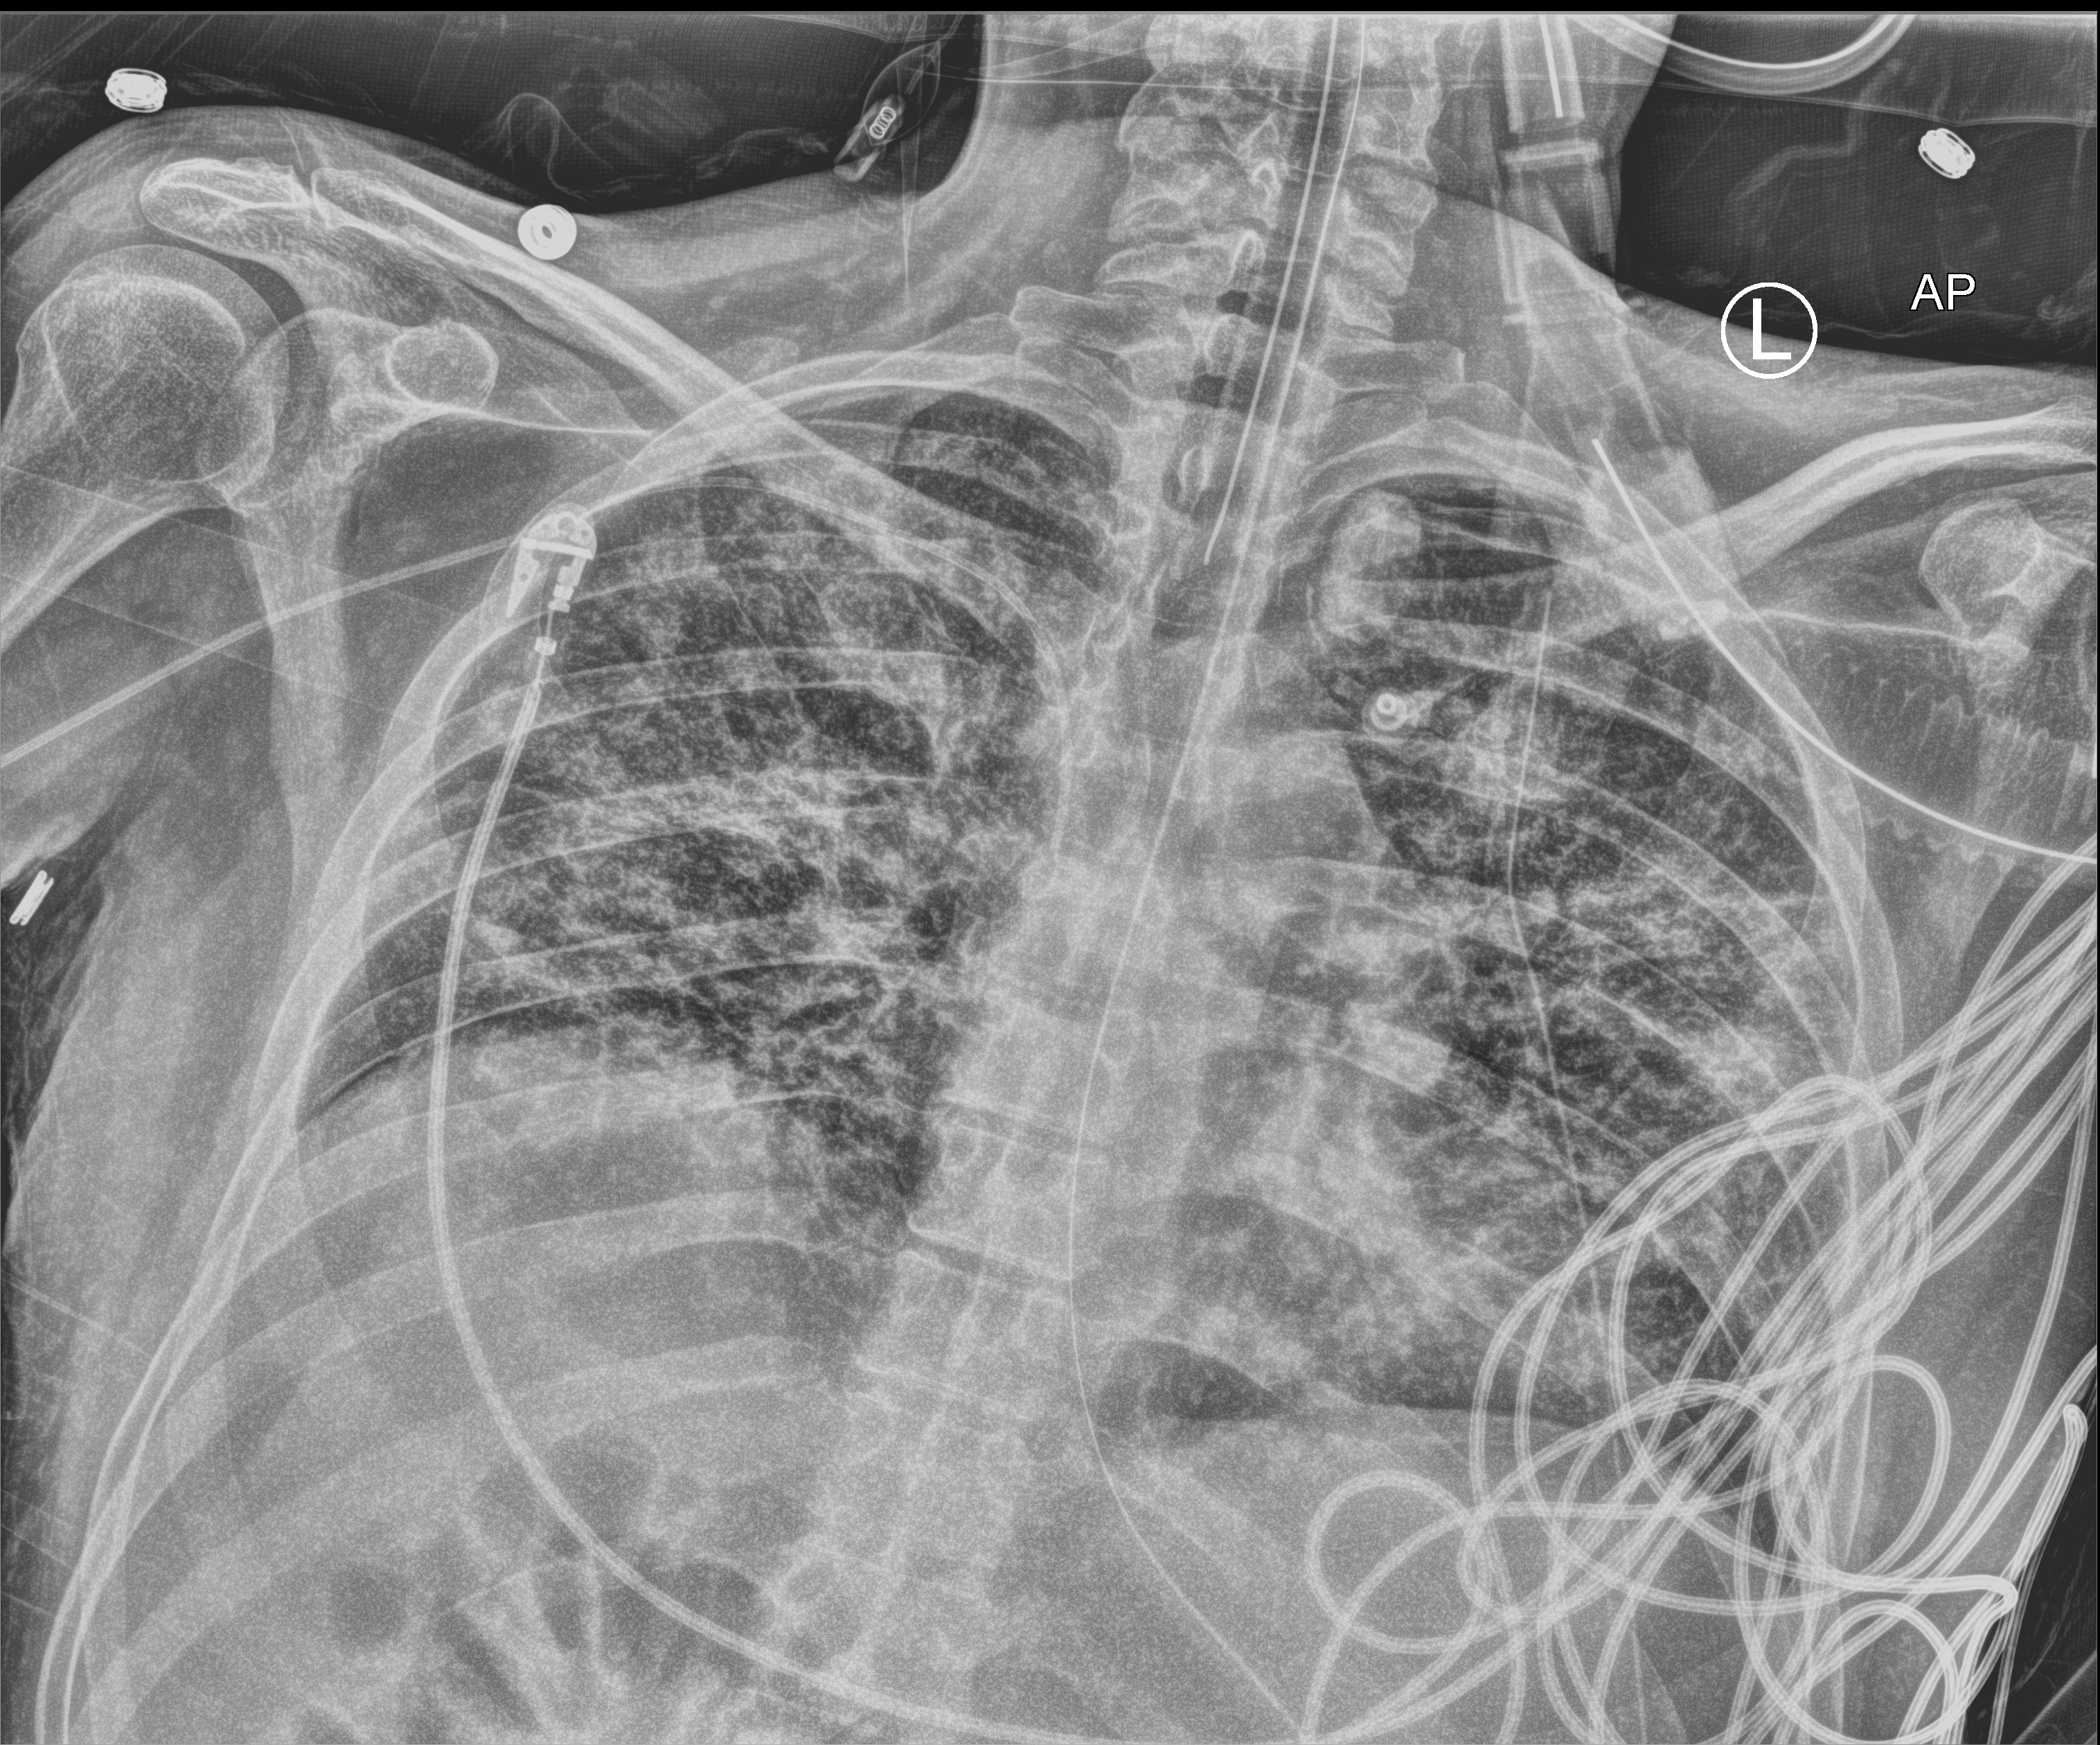
Chest X-ray (portable). Patient hospitalised with COVID-19; male, aged 18–59 years.
Admission-level facts for this patient (not findings on this image; timing relative to this image not recorded):
- chronic kidney disease (admission record): no
- mechanically ventilated during this hospital stay: yes
- admitted to intensive care during this hospital stay: yes